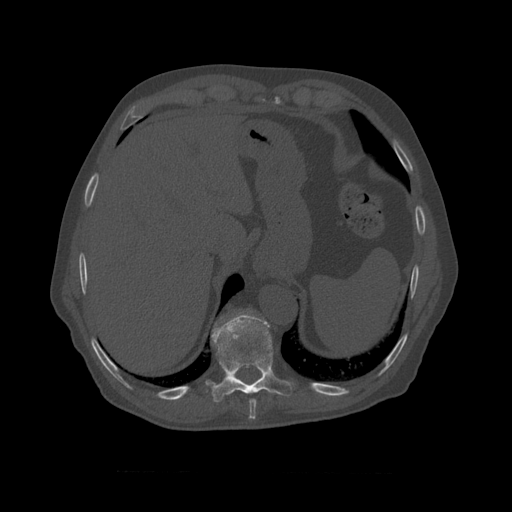
CT including the spine, one axial slice. Slice 424 of 450 in the series (ordered by position). Reconstruction kernel STANDARD. 120 kVp. Bone window (W 1800 / L 400 HU). 1.25 mm slice thickness. 512 × 512 image matrix, field of view 405 × 405 mm. Patient age 75 years. From the clinical record (not read from this slice): primary cancer: prostate.
Annotated regions visible in this slice (semi-automatic segmentation, software-assisted and operator-edited):
- T10 vertebra: box from (x=234, y=310) to (x=252, y=314) px
- T8 vertebra: (x=249, y=399)–(x=257, y=410)
- T9 vertebra: (x=211, y=315)–(x=293, y=397)